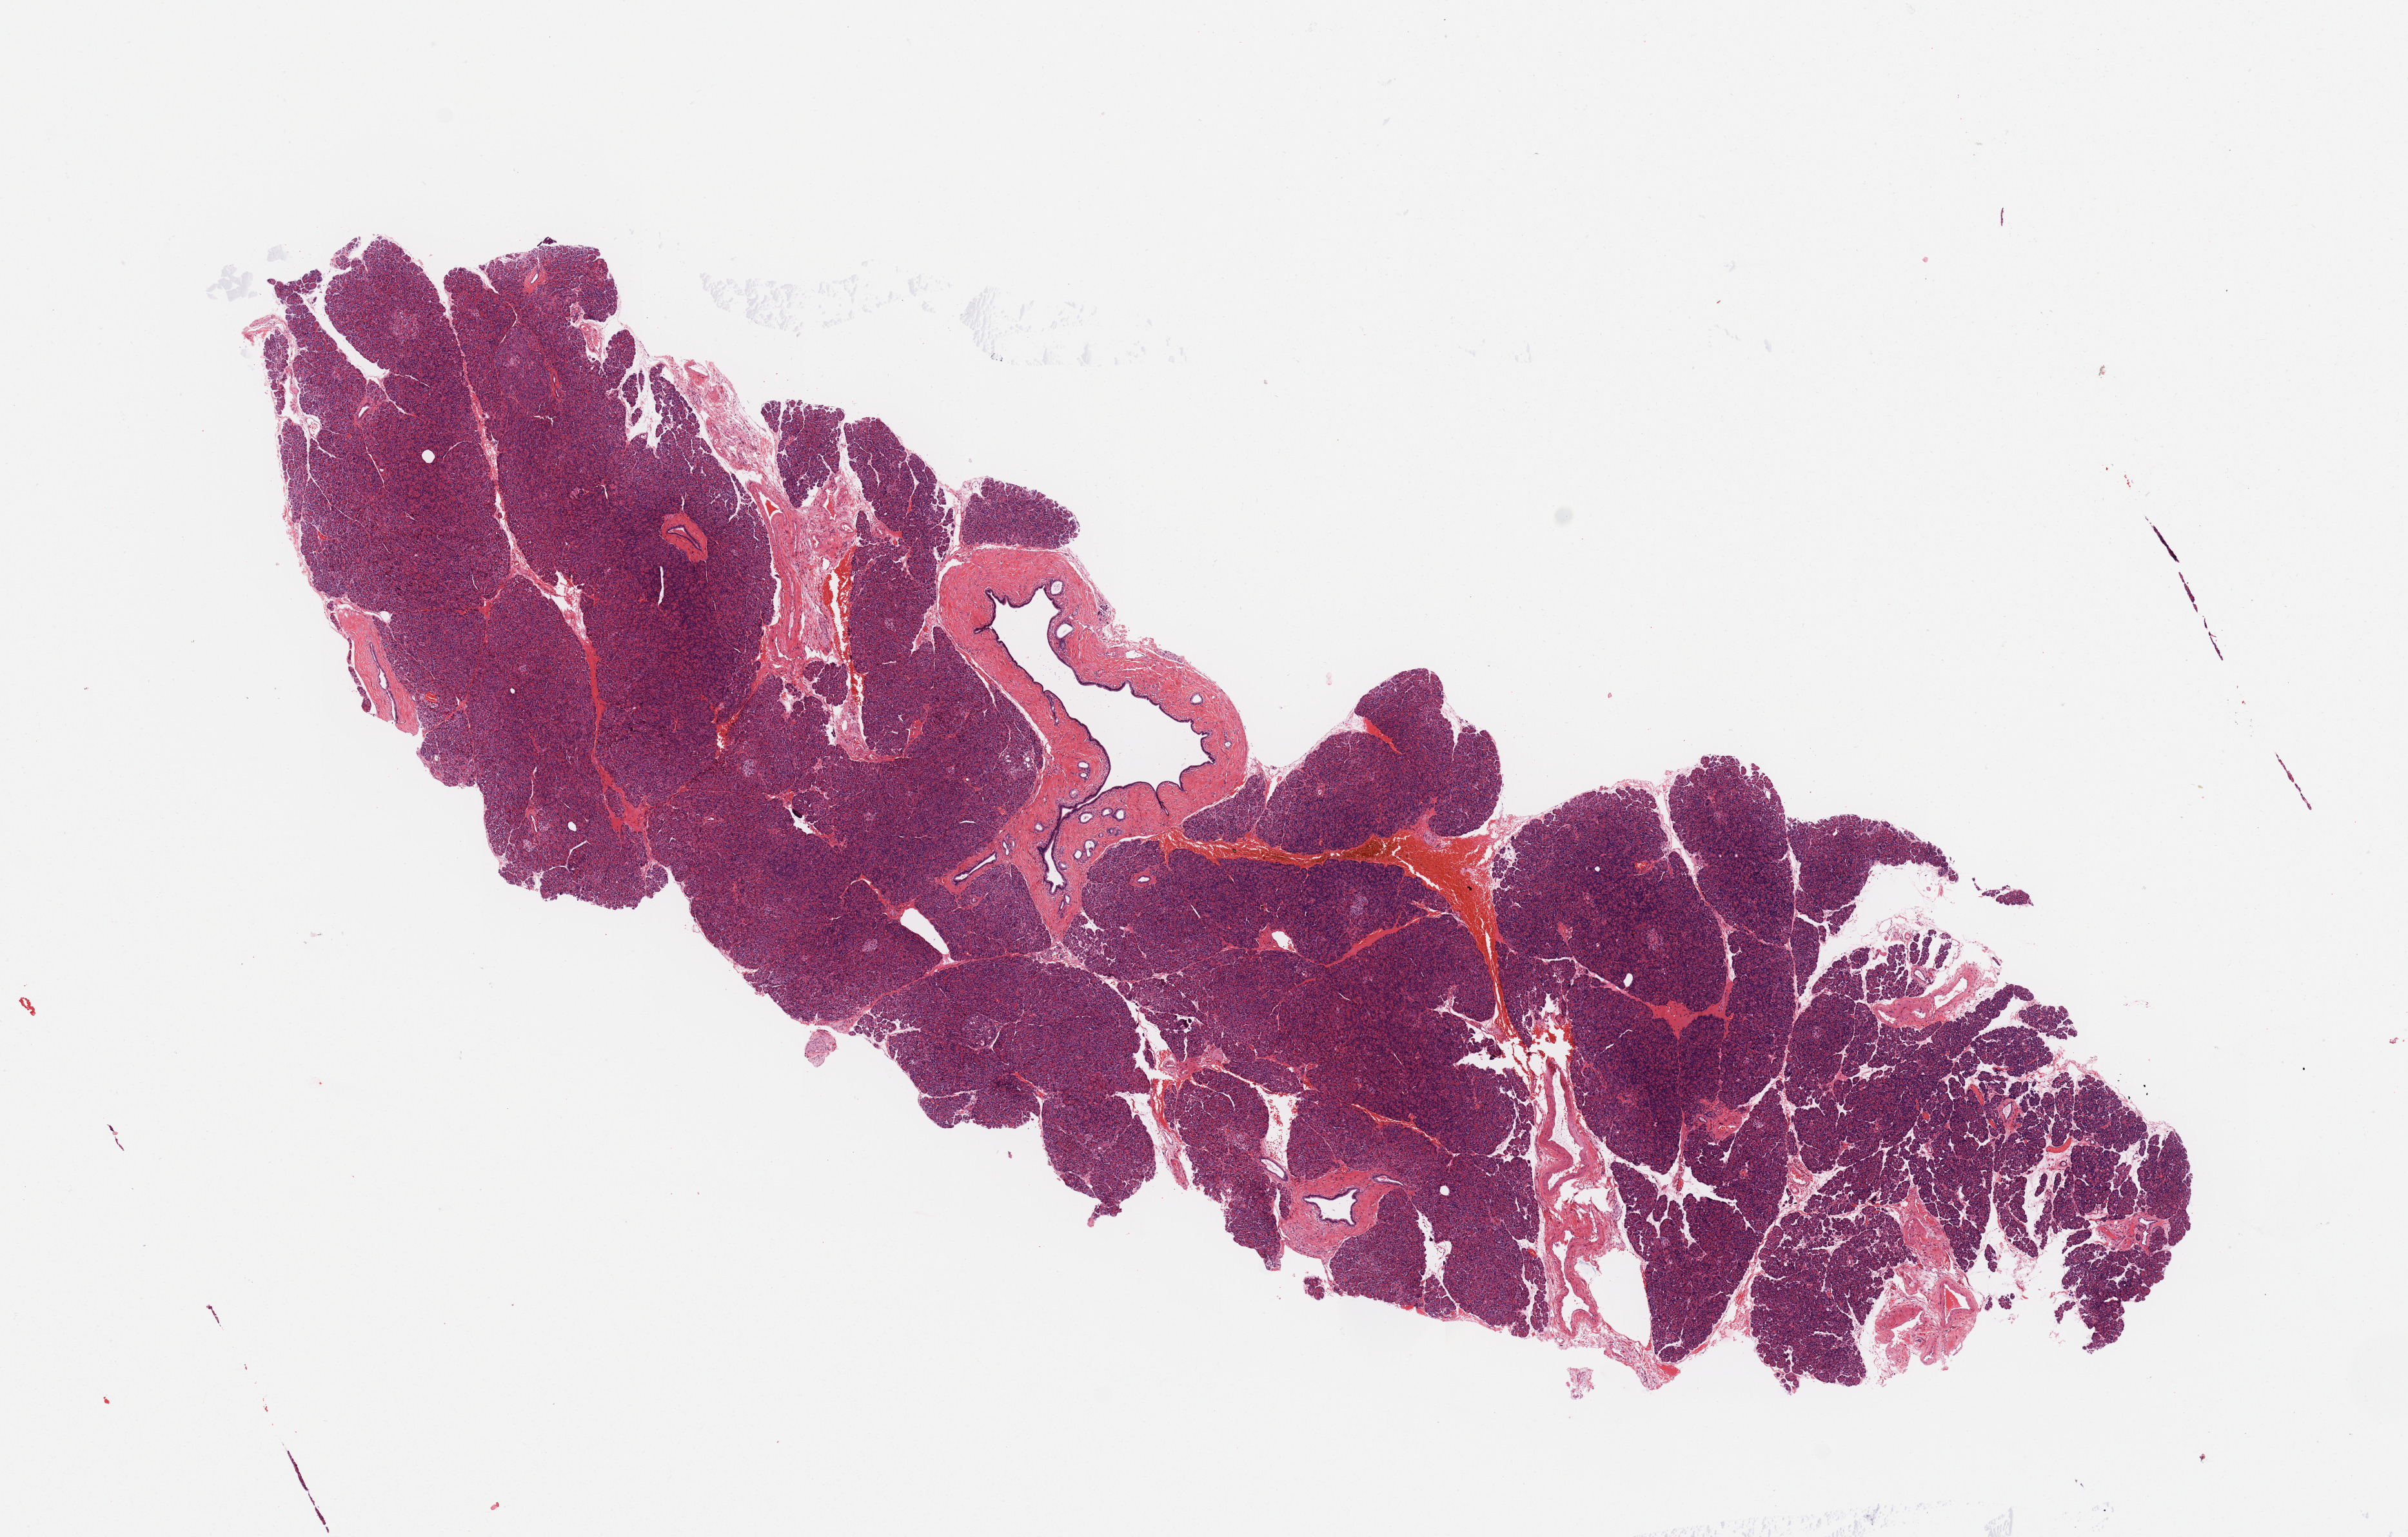
Whole-slide histology image, Hematoxylin and eosin (H&E) stained — a low-resolution overview of the entire scanned area, about 14.8 x 9.4 mm (slide scanned at 20x), normal (non-tumour) tissue sample, sampled site: pancreas. Male, 63 y/o.
• this section: normal (non-tumour) tissue from the same patient
• patient diagnosis: Infiltrating duct carcinoma, NOS